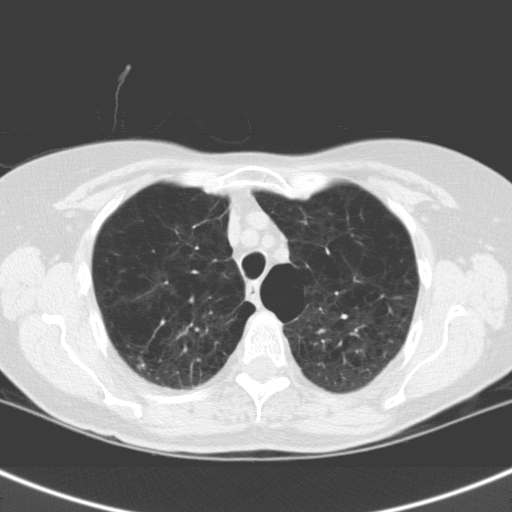
Chest CT (low-dose screening protocol), one axial image, second screening round (one year after baseline), lung window (W 1500 / L -600 HU), 3.2 mm slice thickness, 120 kVp, slice 38 of 158 in the series, 512 × 512 image matrix. Female, age 63 years at enrolment. Current smoker at enrolment.
Expert reader's lesion annotation, bounding box [x1, y1, x2, y2] px = [119, 342, 160, 388]. Reader record for this screening exam (exam-level; its link to the box is not recorded): non-calcified nodule or mass ≥4 mm, right upper lobe, 7 × 7 mm, spiculated (stellate) margins, soft tissue attenuation, pre-existing on the prior screen: no.